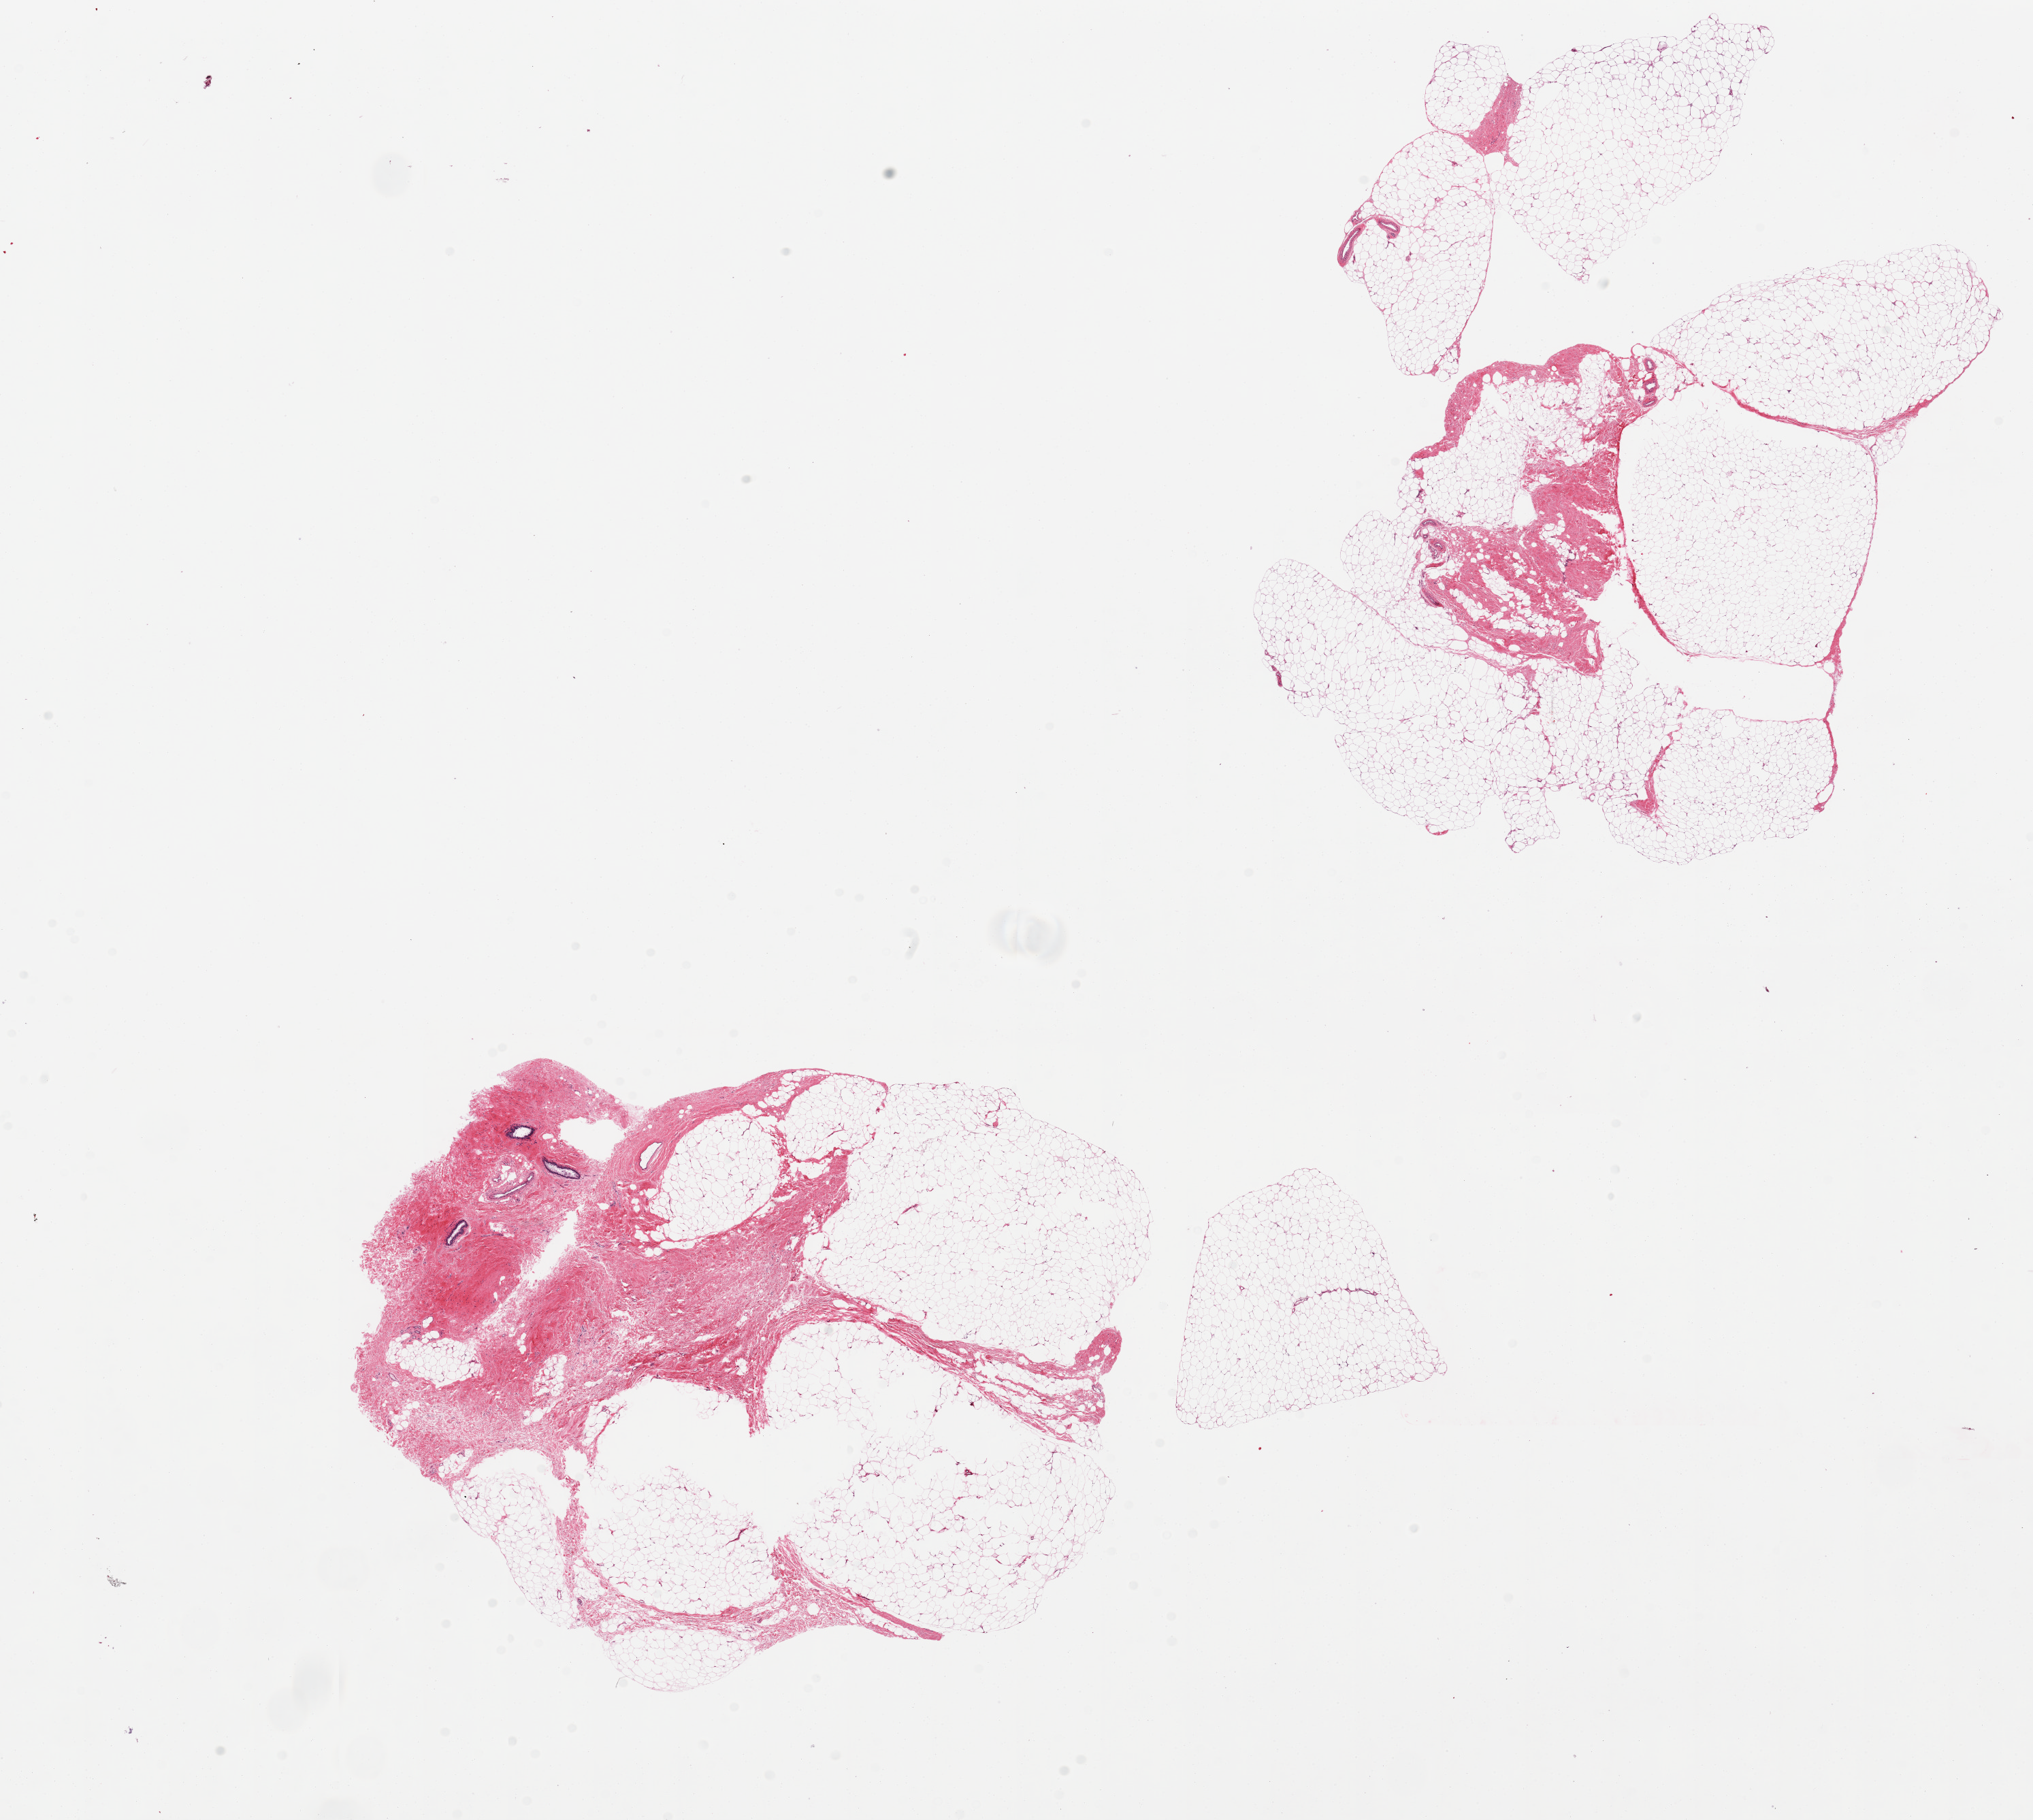
Whole-slide image, hematoxylin and eosin (H&E) stain, brightfield — whole scanned area (about 23.6 x 21.2 mm) shown as a low-resolution overview. PAXgene-fixed, paraffin-embedded tissue. Target tissue: breast. Donor tissue sample. Donor sex: male.
- pathologist's review note for this sample: 2 pieces; mild fibrosis and ductal hyperplasia (gynecomastoid hyperplasia)